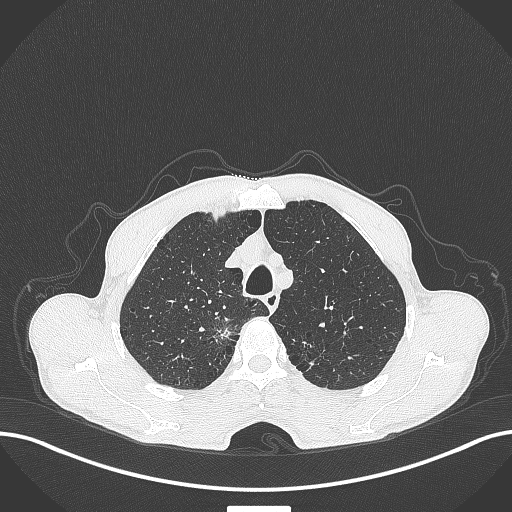
Chest CT, one axial slice; position 344 of 445 along the scan axis; reconstruction kernel B70f; lung window (W 1500 / L -600 HU); 1 mm slice thickness; 512 × 512 image matrix, field of view 400 × 400 mm. Male patient, age 70 years. From the clinical record (not read from this slice): clinical TNM (as recorded): T1a N0 M0; histopathological grade: G1-2.
Outlined on this slice (bounding box drawn by a radiologist):
- lung tumour (recorded histology: adenocarcinoma): bounding box <212,321,244,351> (left, top, right, bottom; pixels)